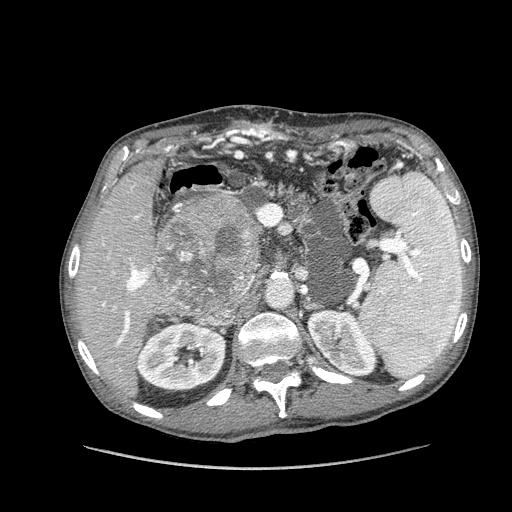
Contrast-enhanced abdominal CT (liver protocol), one axial slice; slice 71 of 162 in the series (ordered by position); reconstruction kernel STANDARD; 100 kVp; soft-tissue window (W 400 / L 40 HU); 512 × 512 image matrix. Case-level facts recorded for this patient, not image findings: diagnosis: hepatocellular carcinoma (patient treated with transarterial chemoembolisation; whether this scan precedes or follows treatment is not stated here); TNM stage (as recorded): Stage-IIIA; Child-Pugh class: A; tumour size: 9.9 cm.
Annotated regions visible in this slice (semi-automatic segmentation, software-assisted and operator-edited):
- liver parenchyma outside the tumour (the mass and vessels are separate outlines, so this box may not span the whole liver): bounding box (x1, y1, x2, y2) in pixels: (76, 158, 248, 396)
- mass: (154, 196, 261, 313)
- liver vessels: (93, 215, 151, 347)